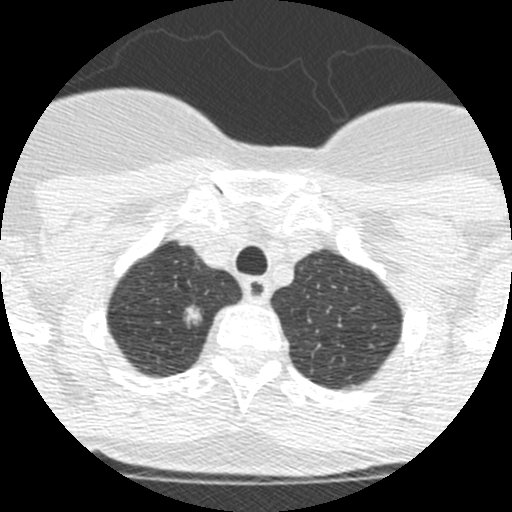
Low-dose screening chest CT, one axial slice. Reconstruction kernel STANDARD. 120 kVp. Lung window (W 1500 / L -600 HU). 512 × 512 image matrix, field of view 257 × 257 mm.
Outlined on this slice (outlined manually by an expert reader):
- lesion 1 (tumor, upper lobe of right lung): bounding box [x1, y1, x2, y2] px = [185, 305, 202, 325]